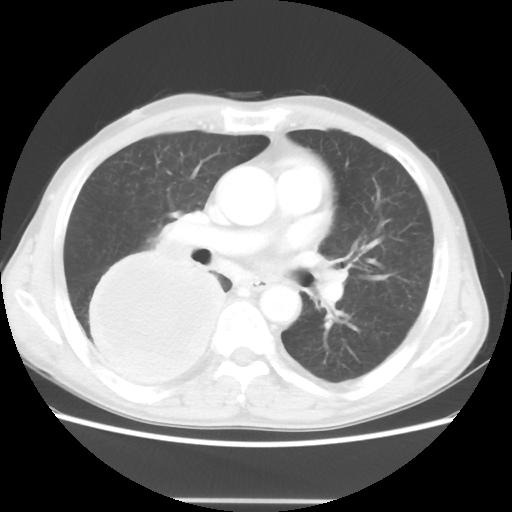
Chest CT, one axial slice; position 25 of 48 along the scan axis; lung window (W 1500 / L -600 HU); 5 mm slice thickness; 512 × 512 image matrix. Patient: male, 66 years. From the clinical record (not read from this slice): clinical TNM (as recorded): T4 N1 M1.
Outlined on this slice (rectangle marked by the reading radiologist):
- lung tumour (recorded histology: small cell carcinoma): bounding box [x1, y1, x2, y2] px = [72, 241, 229, 390]